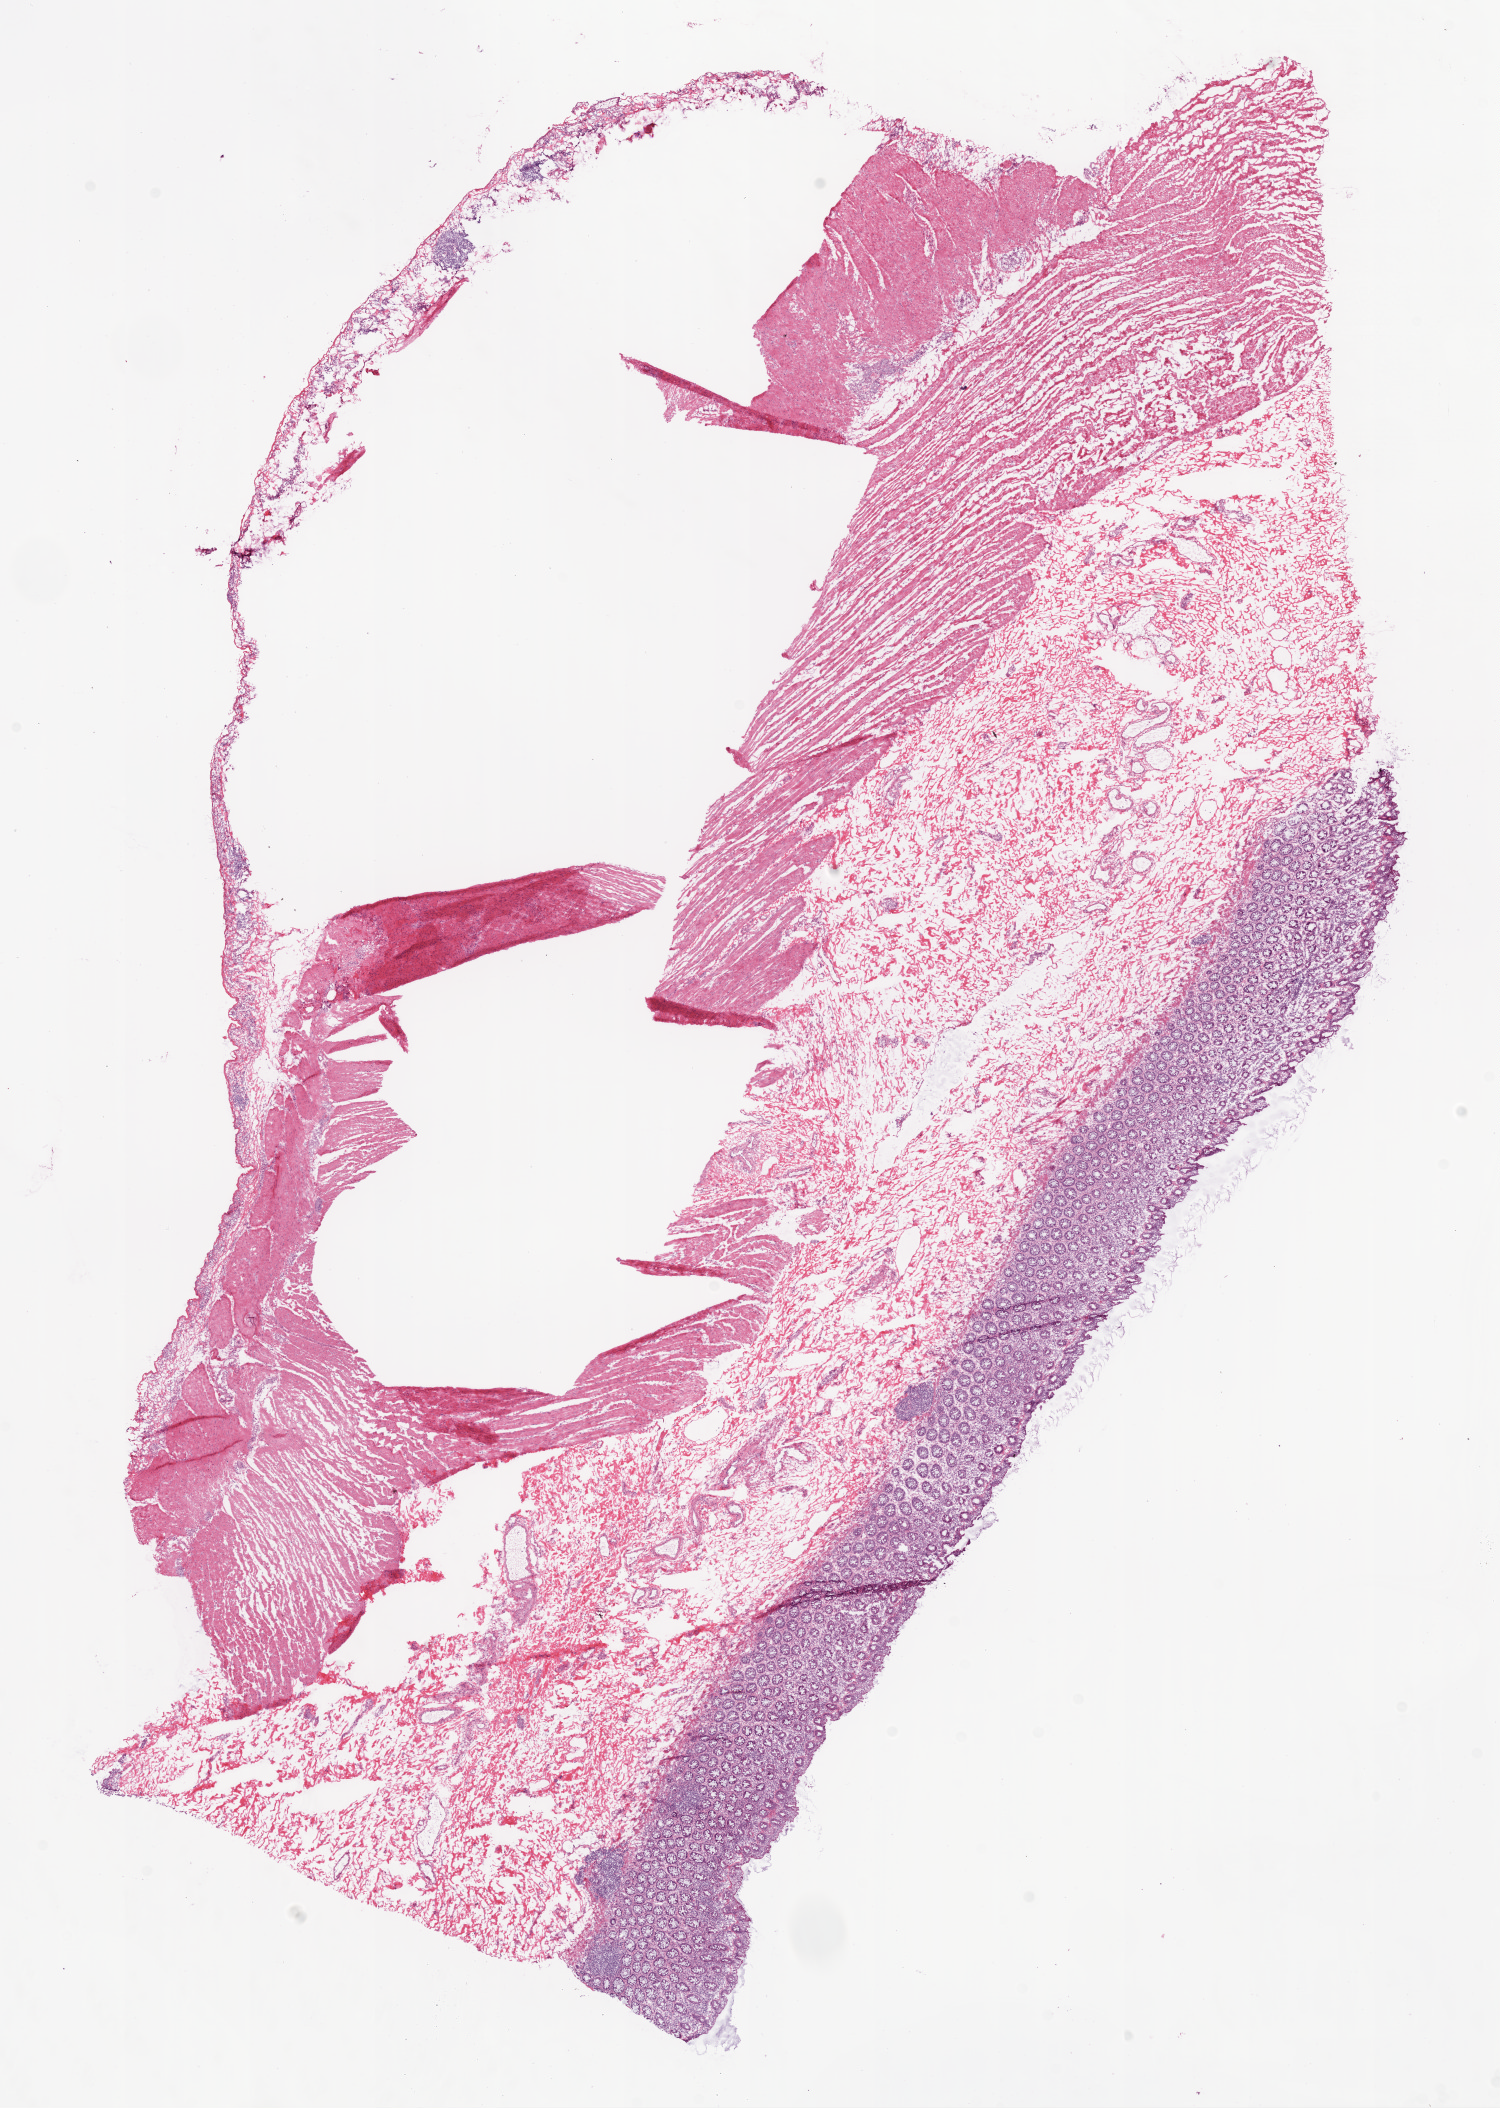
Whole-slide histology image, H&E — low-resolution overview of the scanned area, about 12.0 x 16.9 mm (slide scanned at 20x). Frozen section from the bottom of the tissue portion. Sample: solid tissue normal (non-tumour tissue), ovary. Female, age 63 years at initial diagnosis.
This section: solid tissue normal sample (biorepository sample class). Patient diagnosis: Serous cystadenocarcinoma, NOS.